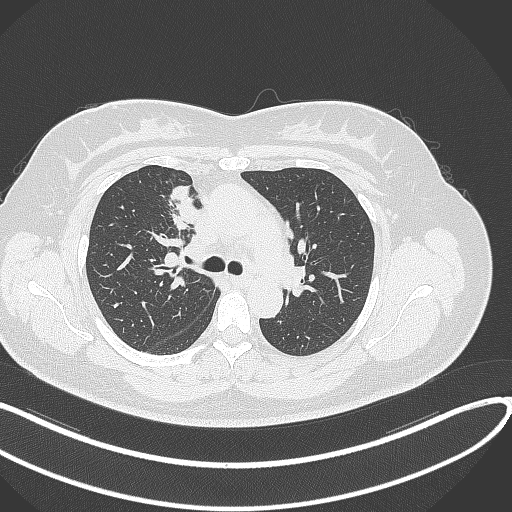
Chest CT, one axial slice. Slice 185 of 303 in the series (ordered by position). Reconstruction kernel B70f. Lung window (W 1500 / L -600 HU). 1 mm slice thickness. 512 × 512 image matrix, field of view 400 × 400 mm. Patient: female, 46 years. From the clinical record (not read from this slice): clinical TNM (as recorded): T2a N1 M0.
Outlined on this slice (rectangle marked by the reading radiologist):
- lung tumour (recorded histology: adenocarcinoma): box from (x=167, y=186) to (x=199, y=231) px